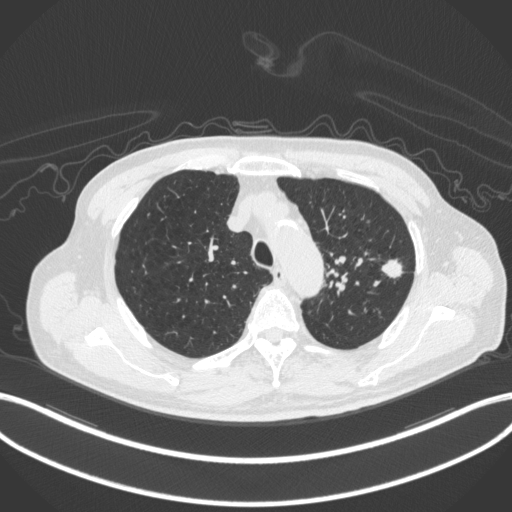
Chest CT, one axial slice; position 342 of 420 along the scan axis; reconstruction kernel B31f; 120 kVp; lung window (W 1500 / L -600 HU); 1 mm slice thickness; 512 × 512 image matrix, field of view 400 × 400 mm. Male patient, age 77 years. Case-level facts recorded for this patient, not image findings: clinical TNM (as recorded): T3 N1 M0.
Annotated regions visible in this slice (rectangle marked by the reading radiologist):
- lung tumour (recorded histology: adenocarcinoma): bounding box <378,252,406,280> (left, top, right, bottom; pixels)